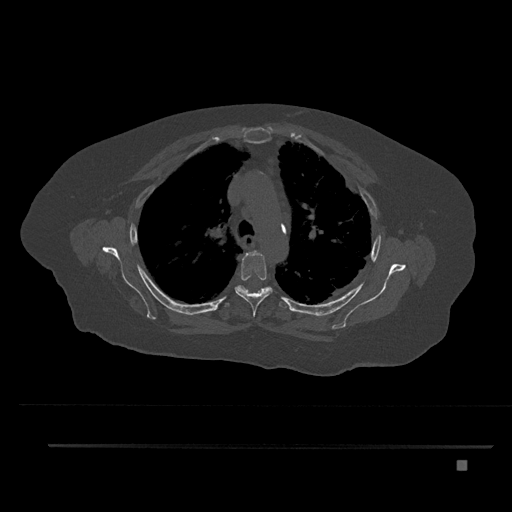
CT including the spine, one axial slice. Bone window (W 1800 / L 400 HU). 0.5 mm slice thickness. 512 × 512 image matrix, field of view 437 × 437 mm. Female patient, age 76 years. From the clinical record (not read from this slice): primary cancer: lung.
Structures marked on this image (semi-automatic segmentation, software-assisted and operator-edited):
- T3 vertebra: bounding box <244,251,257,258> (left, top, right, bottom; pixels)
- T4 vertebra: <235,250,272,317>
- T5 vertebra: <226,285,290,308>